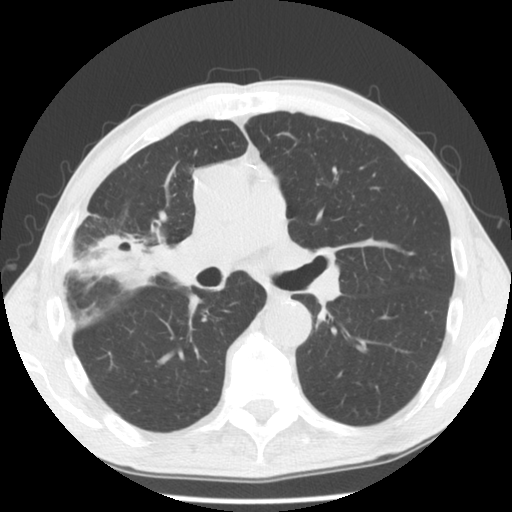
Low-dose screening chest CT, one axial slice. Slice 76 of 132 in the series (ordered by position). 140 kVp. Lung window (W 1500 / L -600 HU). 2.5 mm slice thickness. 512 × 512 image matrix, field of view 334 × 334 mm.
Structures marked on this image (expert manual segmentation):
- lesion 1 (tumor, hilum of right lung): bounding box (x1, y1, x2, y2) in pixels: (123, 243, 173, 284)